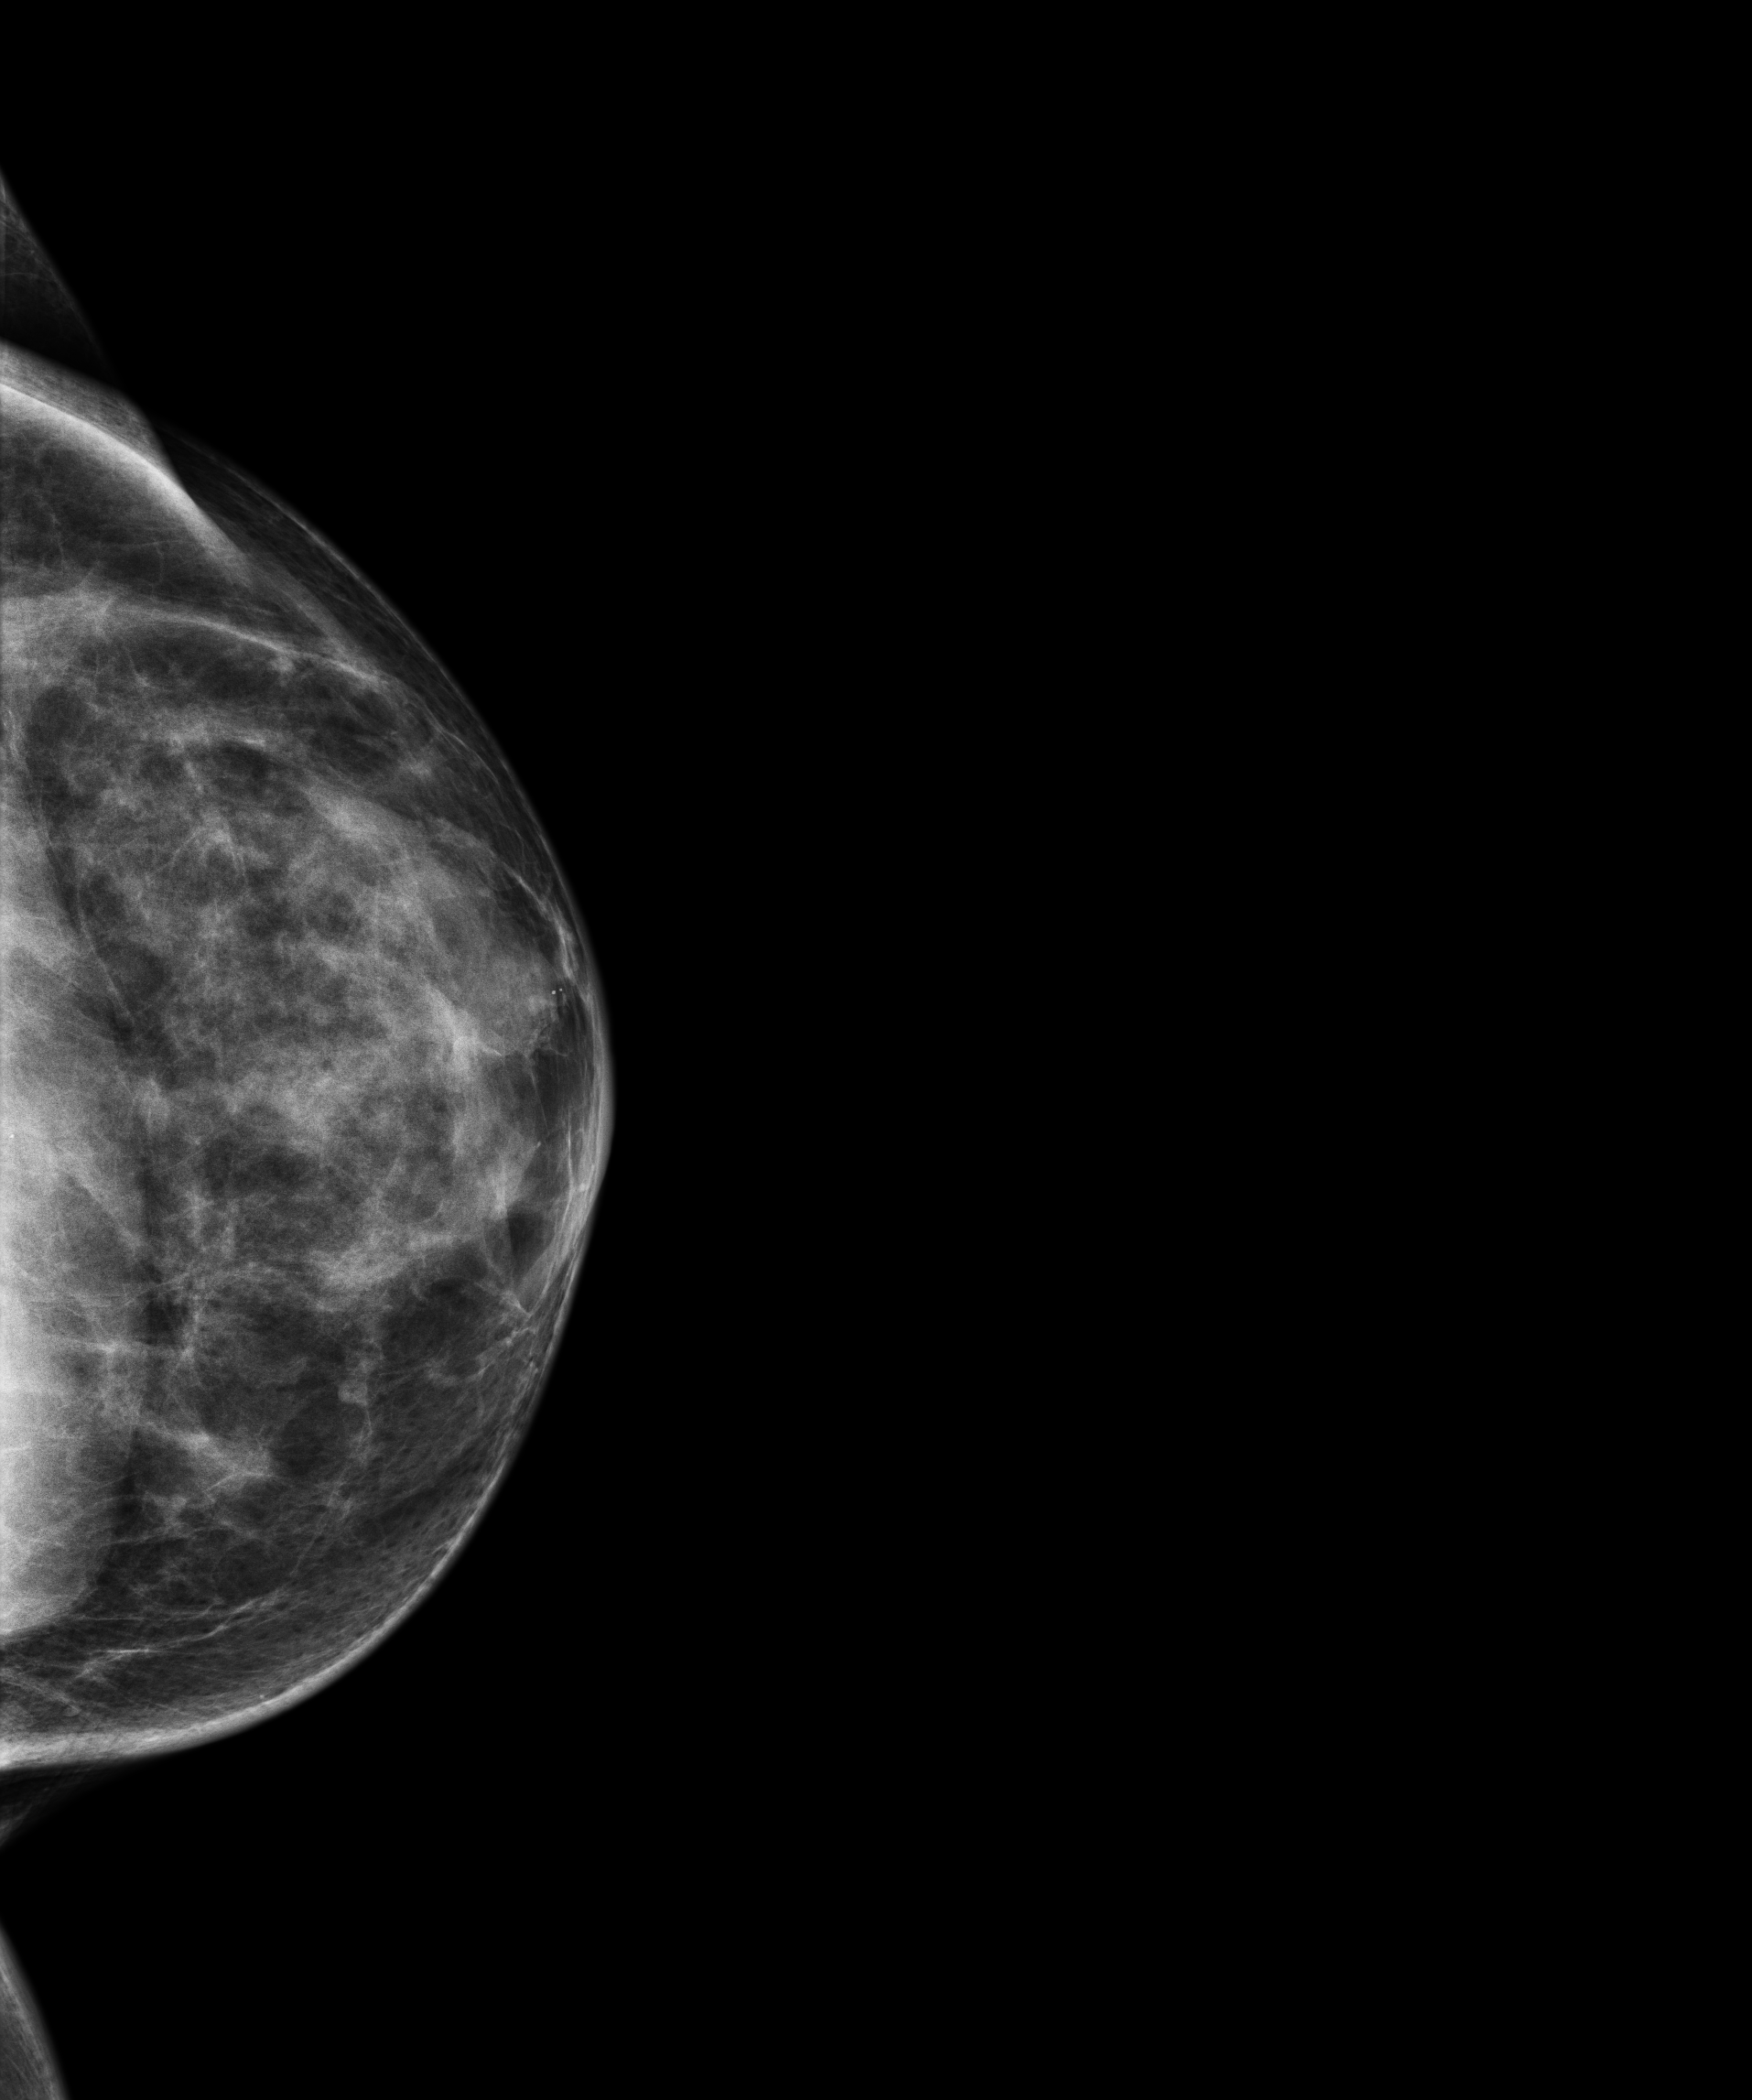
Digital mammogram (FFDM), left breast, craniocaudal (CC) view, screening examination, compressed breast thickness 61 mm. Patient aged 66 years (female).
BI-RADS breast density category at the screening exam (both breasts, scale 1–4): 3. Final BI-RADS assessment for this screening round (tomosynthesis exam, both breasts): category 1. Recall: no recall after this screen.